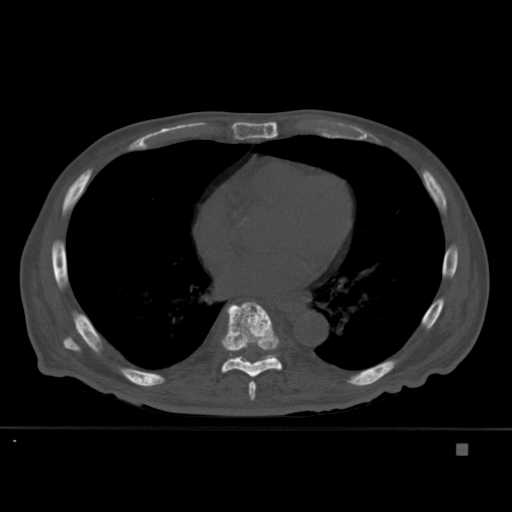
CT including the spine, one axial slice. Slice 263 of 451 in the series (ordered by position). Bone window (W 1800 / L 400 HU). 512 × 512 image matrix, field of view 378 × 378 mm. Male patient, age 75 years. Case-level facts recorded for this patient, not image findings: primary cancer: prostate.
Outlined on this slice (semi-automatic segmentation, software-assisted and operator-edited):
- T7 vertebra: bounding box [x1, y1, x2, y2] px = [249, 380, 257, 400]
- T8 vertebra: [221, 302, 282, 377]
- T9 vertebra: [229, 353, 277, 361]